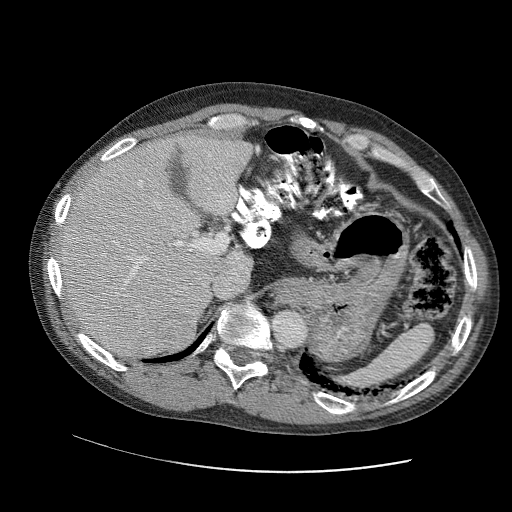
Contrast-enhanced abdominal CT (liver protocol), one axial slice. Slice 72 of 109 in the series (ordered by position). Reconstruction kernel STANDARD. Soft-tissue window (W 400 / L 40 HU). 2.5 mm slice thickness. 512 × 512 image matrix. Case-level facts recorded for this patient, not image findings: diagnosis: hepatocellular carcinoma (patient treated with transarterial chemoembolisation; whether this scan precedes or follows treatment is not stated here); TNM stage (as recorded): Stage-IIIC; Child-Pugh class: B; tumour differentiation: well differentiated; tumour nodularity: uninodular.
Structures marked on this image (semi-automatic segmentation, software-assisted and operator-edited):
- liver parenchyma outside the tumour (the mass and vessels are separate outlines, so this box may not span the whole liver): box from (x=56, y=129) to (x=252, y=359) px
- mass: (x=156, y=315)–(x=196, y=351)
- liver vessels: (x=99, y=143)–(x=250, y=337)